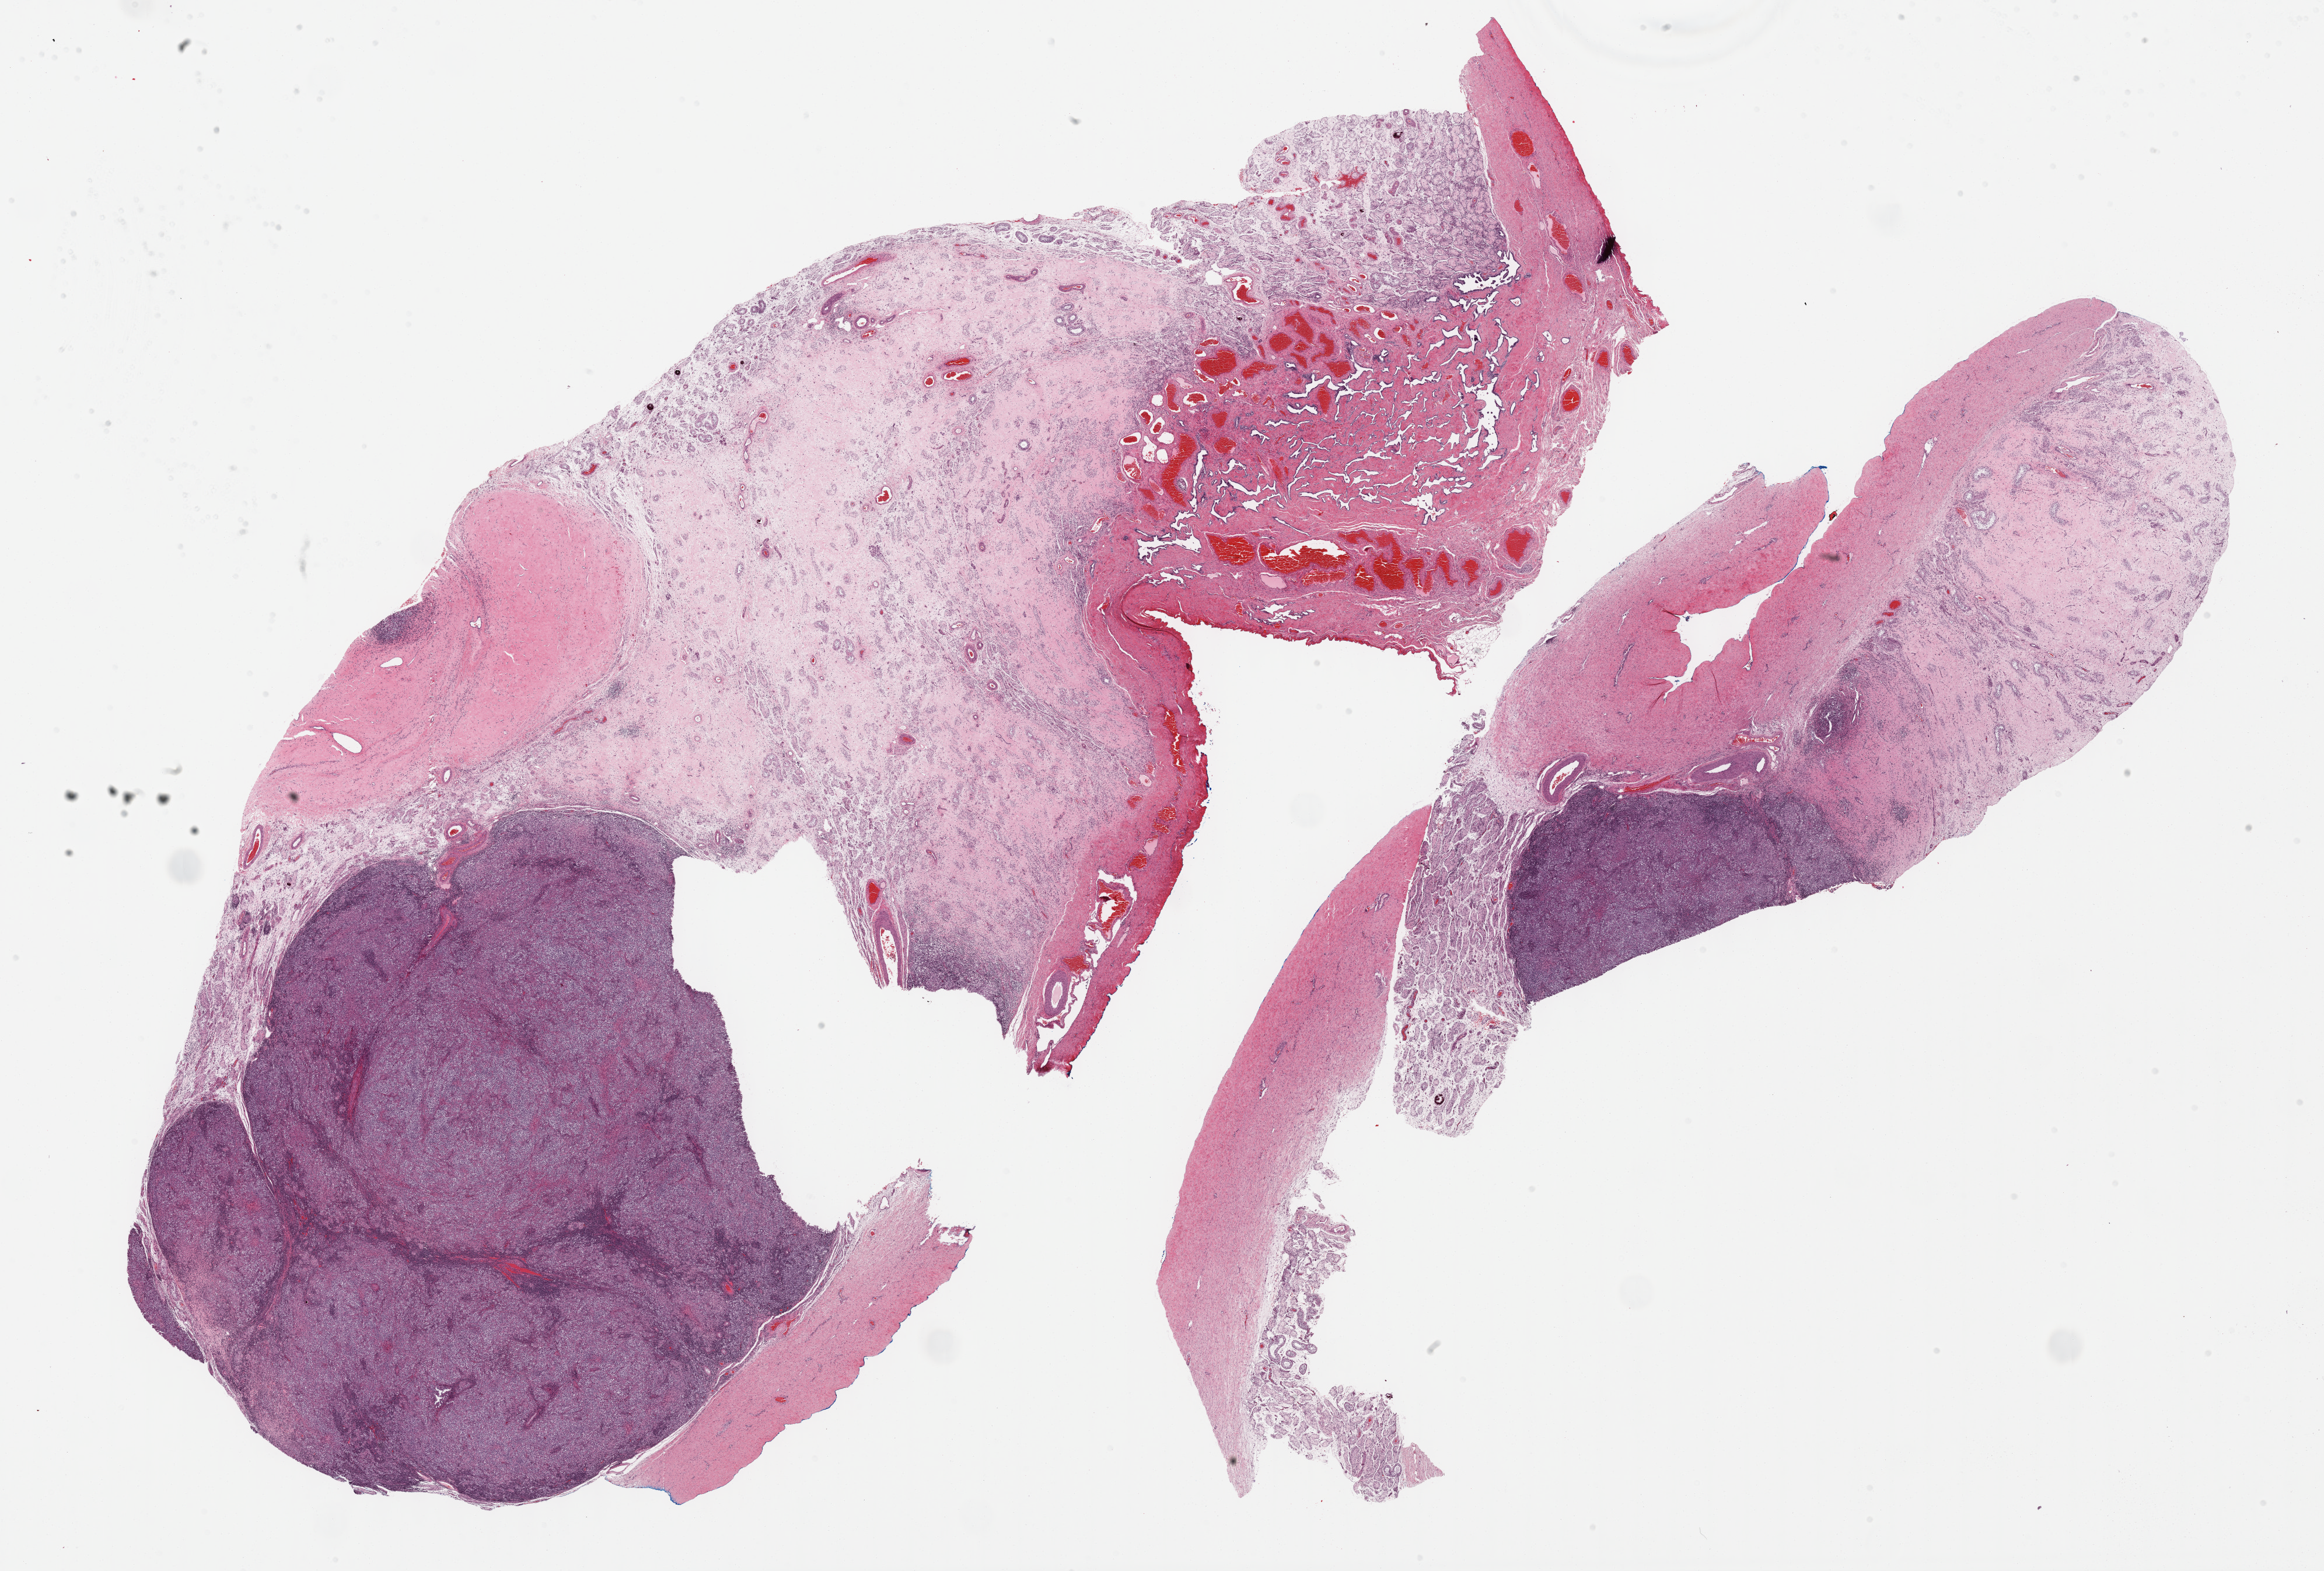
Digitized H&E tissue section (whole slide), whole scanned area (about 32.2 x 21.8 mm) shown as a low-resolution overview. FFPE section. Primary tumour sample from the testis. Patient: male, age at initial diagnosis 35 years.
Laterality: right. AJCC pathologic stage: IA (7th edition). Pathologic diagnosis: Seminoma, NOS.